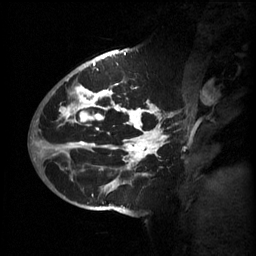
Breast MRI (dynamic contrast-enhanced), one sagittal slice. Position 37 of 60 along the scan axis. 3 images stored at this slice position (order not interpretable as contrast timing). 1.5 T. TE 4.2 ms, TR 11 ms. 256 × 256 image matrix, field of view 220 × 220 mm. Female patient, age 51 years.
Structures marked on this image (semi-automatically segmented with operator editing):
- analysis volume of interest (the breast-tissue region the enhancement analysis was run in; not a lesion): bounding box <63,80,179,201> (left, top, right, bottom; pixels)
- tumour enhancement mask (voxels above the 70 % enhancement threshold inside the analysis volume of interest): <63,80,174,195>